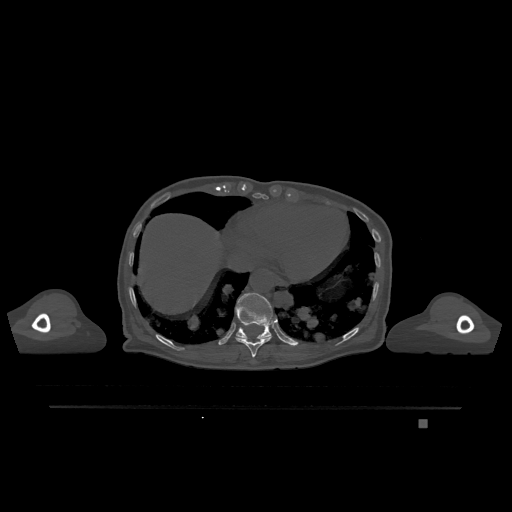
CT including the spine, one axial slice; position 619 of 1317 along the scan axis; bone window (W 1800 / L 400 HU); 0.5 mm slice thickness; 512 × 512 image matrix, field of view 500 × 500 mm. Patient: female, 74 years. From the clinical record (not read from this slice): primary cancer: lung; vertebrae with lytic lesions (as recorded): T1, T4, T5, T6, L4, L5.
Structures marked on this image (semi-automatically segmented with operator editing):
- T10 vertebra: bounding box <236,337,272,358> (left, top, right, bottom; pixels)
- T11 vertebra: <235,293,277,339>